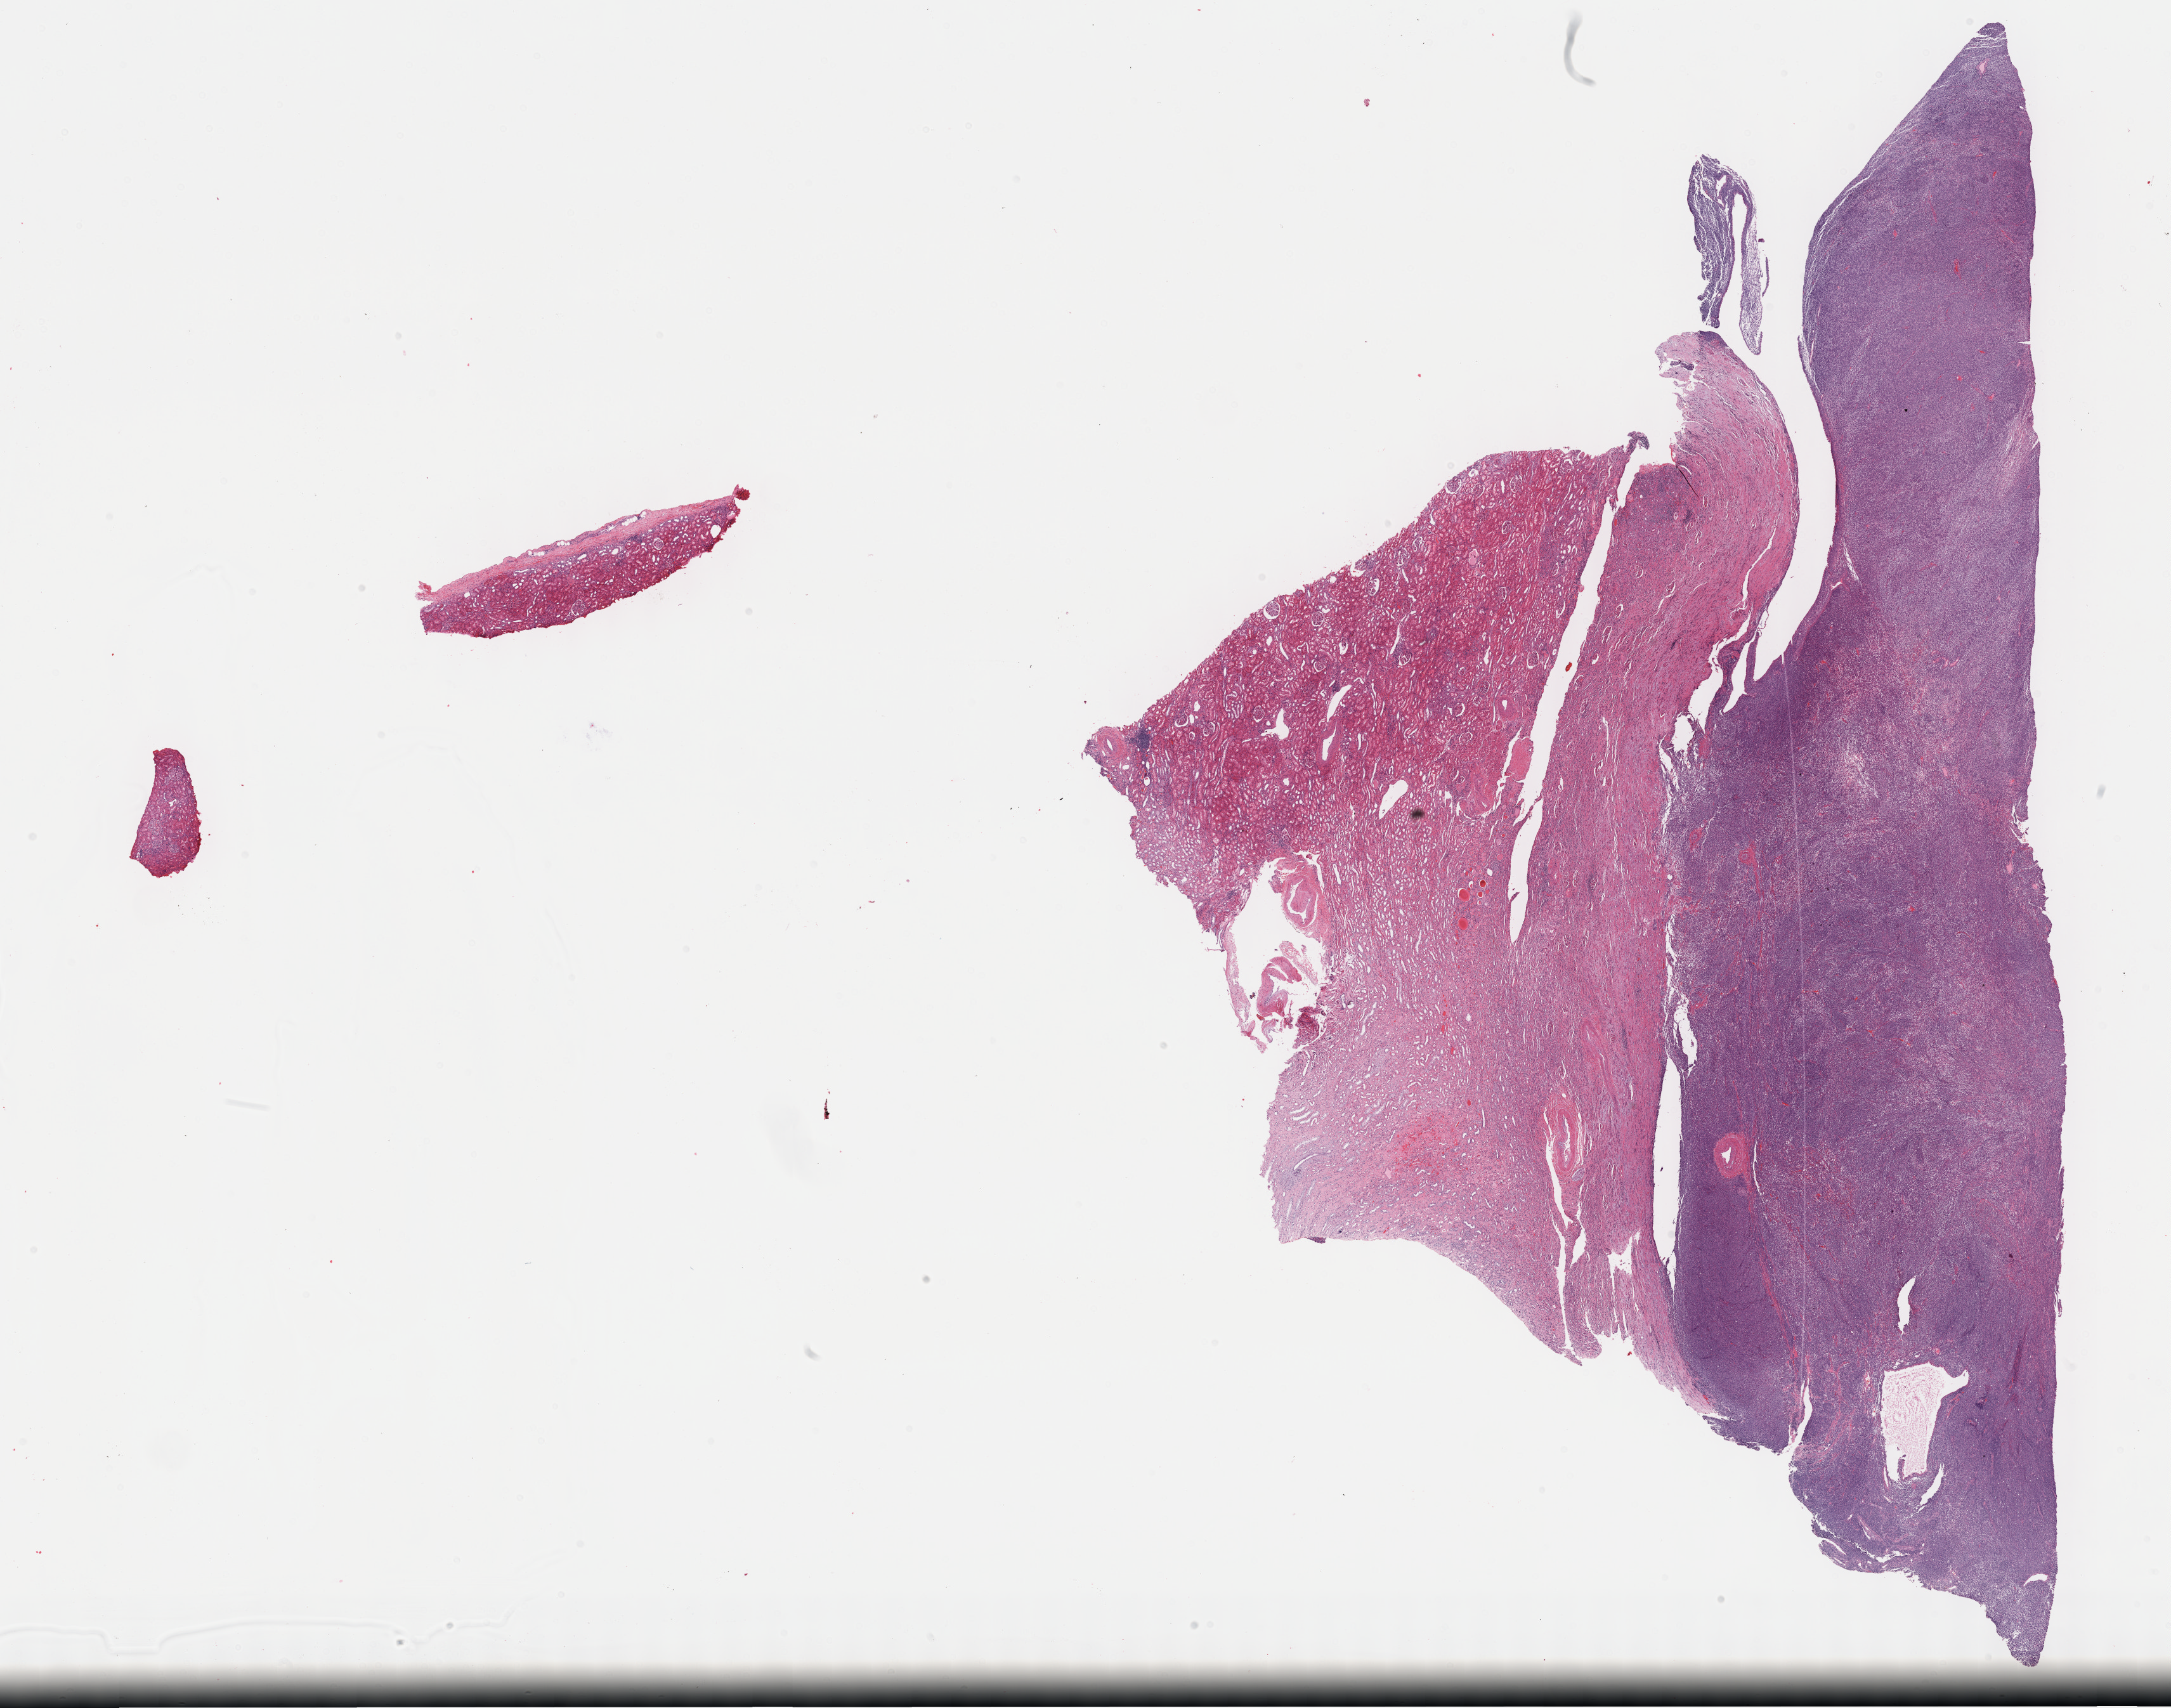
H&E-stained whole-slide image — whole scanned area (about 27.7 x 21.8 mm) shown as a low-resolution overview. FFPE section. Kidney, primary tumour sample. Female patient; age at initial diagnosis 40 years.
Pathologic diagnosis: Synovial sarcoma, spindle cell.